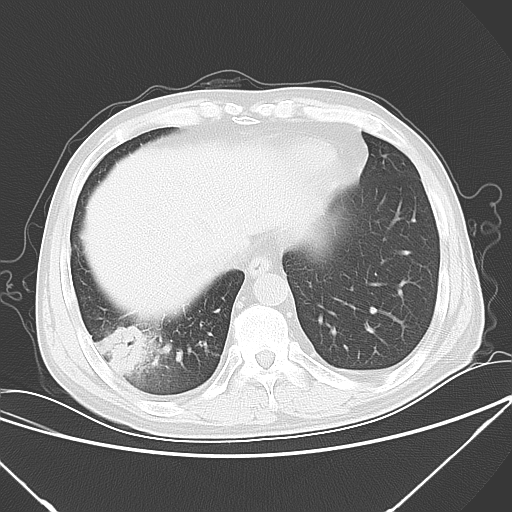
Chest CT, one axial slice; slice 17 of 57 in the series (ordered by position); 120 kVp; lung window (W 1500 / L -600 HU); 5 mm slice thickness; 512 × 512 image matrix. Patient: male, 54 years. Case-level facts recorded for this patient, not image findings: clinical TNM (as recorded): T2 N1 M0; histopathological grade: G3.
Structures marked on this image (bounding box drawn by a radiologist):
- lung tumour (recorded histology: adenocarcinoma): bounding box <94,325,151,377> (left, top, right, bottom; pixels)